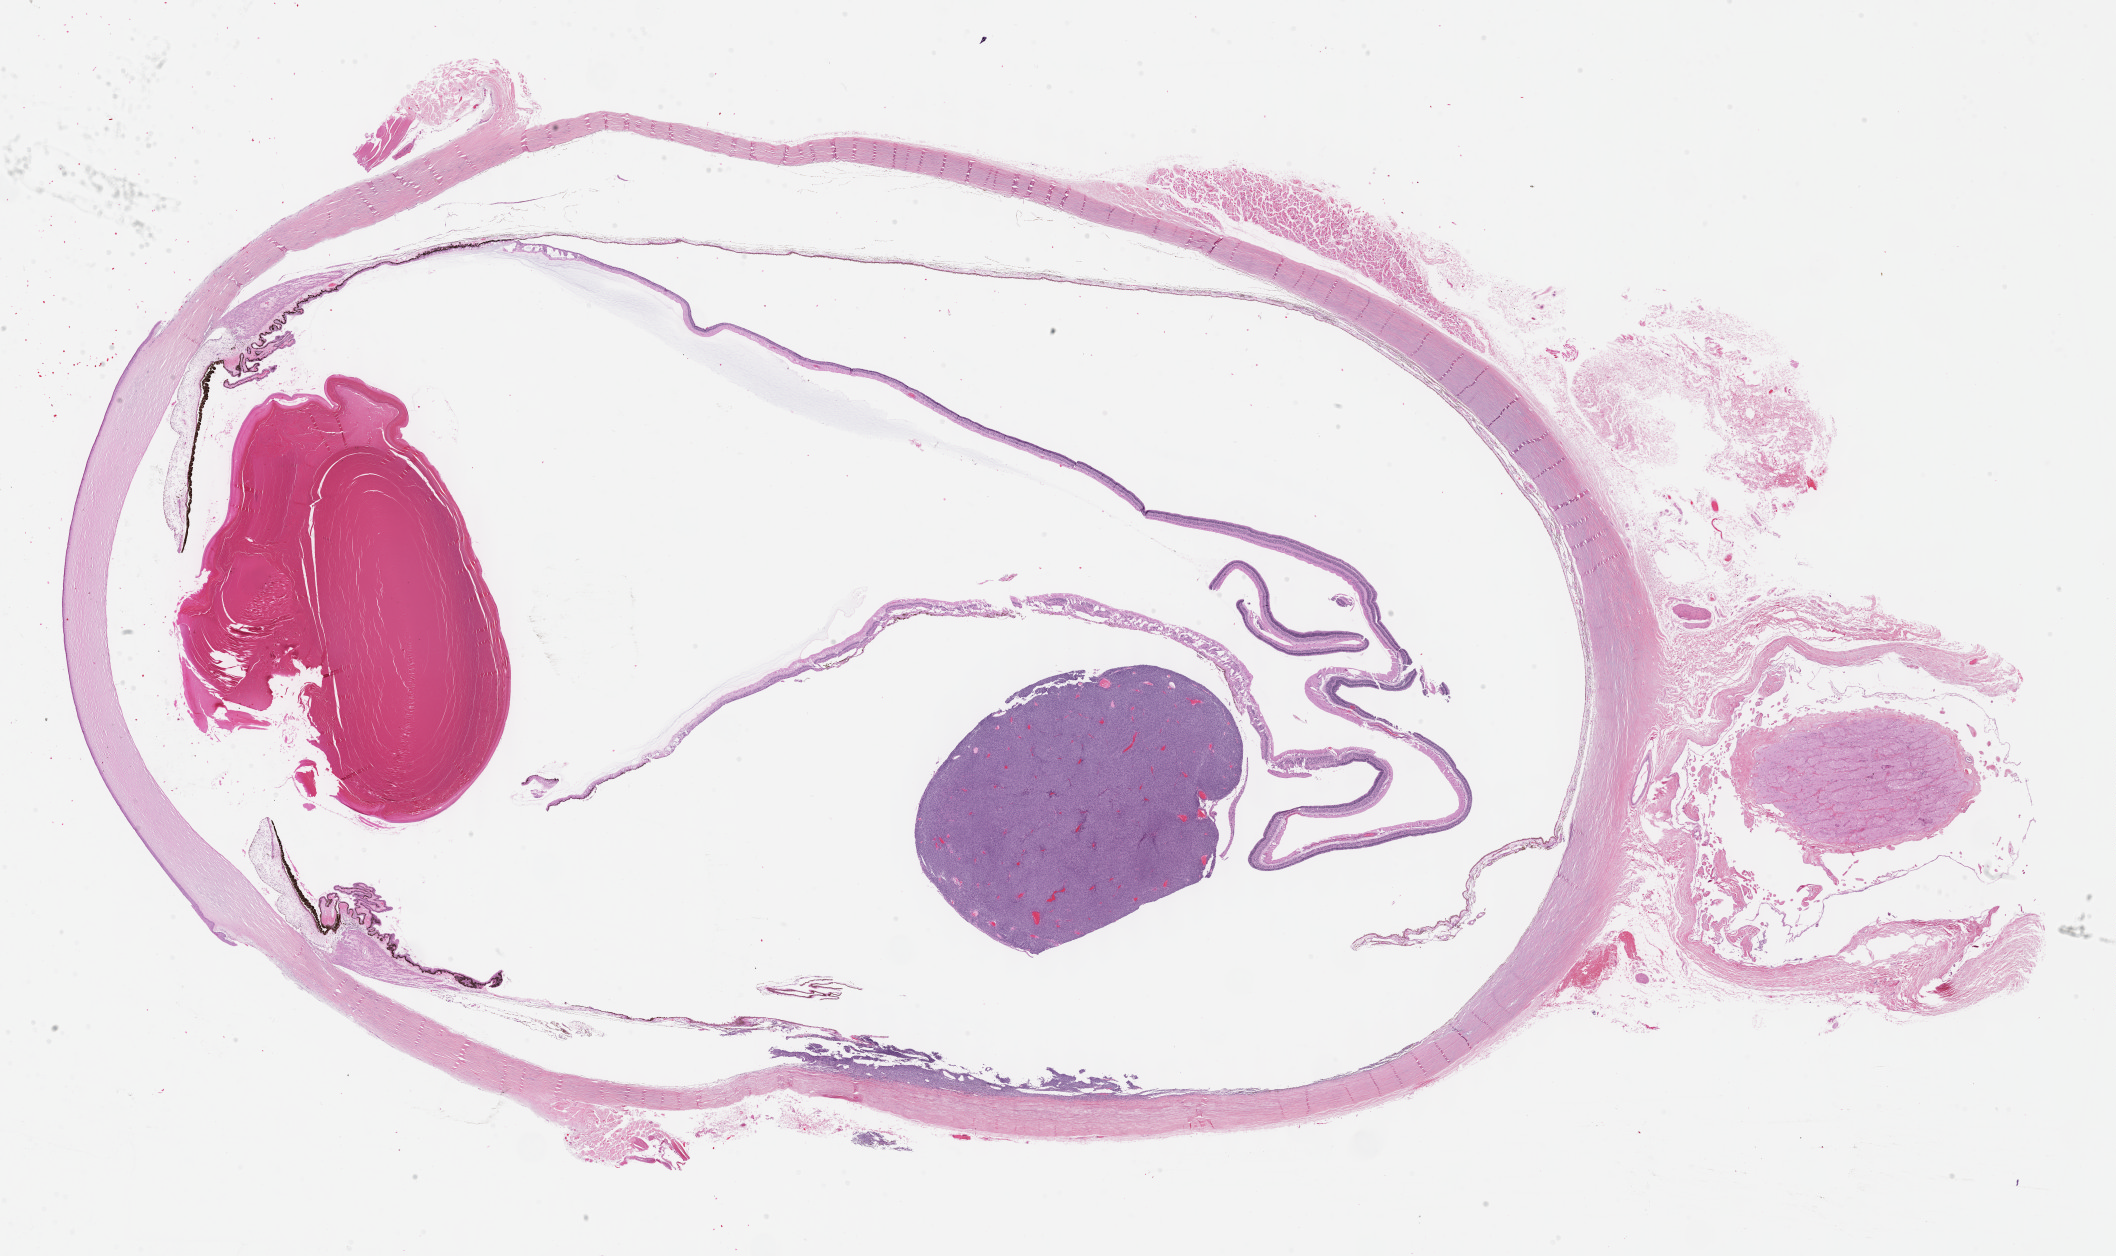
Hematoxylin and eosin (H&E) stained whole-slide image, a low-resolution overview of the entire scanned area, about 34.2 x 20.3 mm (acquisition: 40x scan); formalin-fixed paraffin-embedded (FFPE) diagnostic section; uvea, primary tumour sample. Male patient; age at initial diagnosis 73 years.
Diagnosis: Spindle cell melanoma, type B (overlapping lesion of eye and adnexa). Laterality: right. AJCC pathologic stage: IIIA.